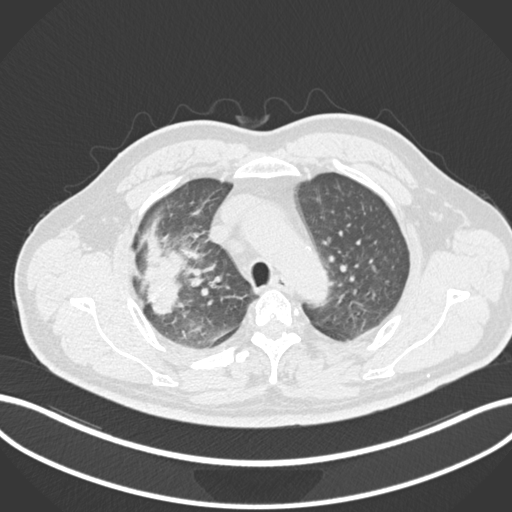
Chest CT, one axial slice; slice 676 of 852 in the series (ordered by position); lung window (W 1500 / L -600 HU); 1 mm slice thickness; 512 × 512 image matrix. Patient: male, 55 years. From the clinical record (not read from this slice): clinical TNM (as recorded): T3 N2 M1.
Outlined on this slice (bounding box drawn by a radiologist):
- lung tumour (recorded histology: adenocarcinoma): bounding box [x1, y1, x2, y2] px = [139, 234, 186, 318]